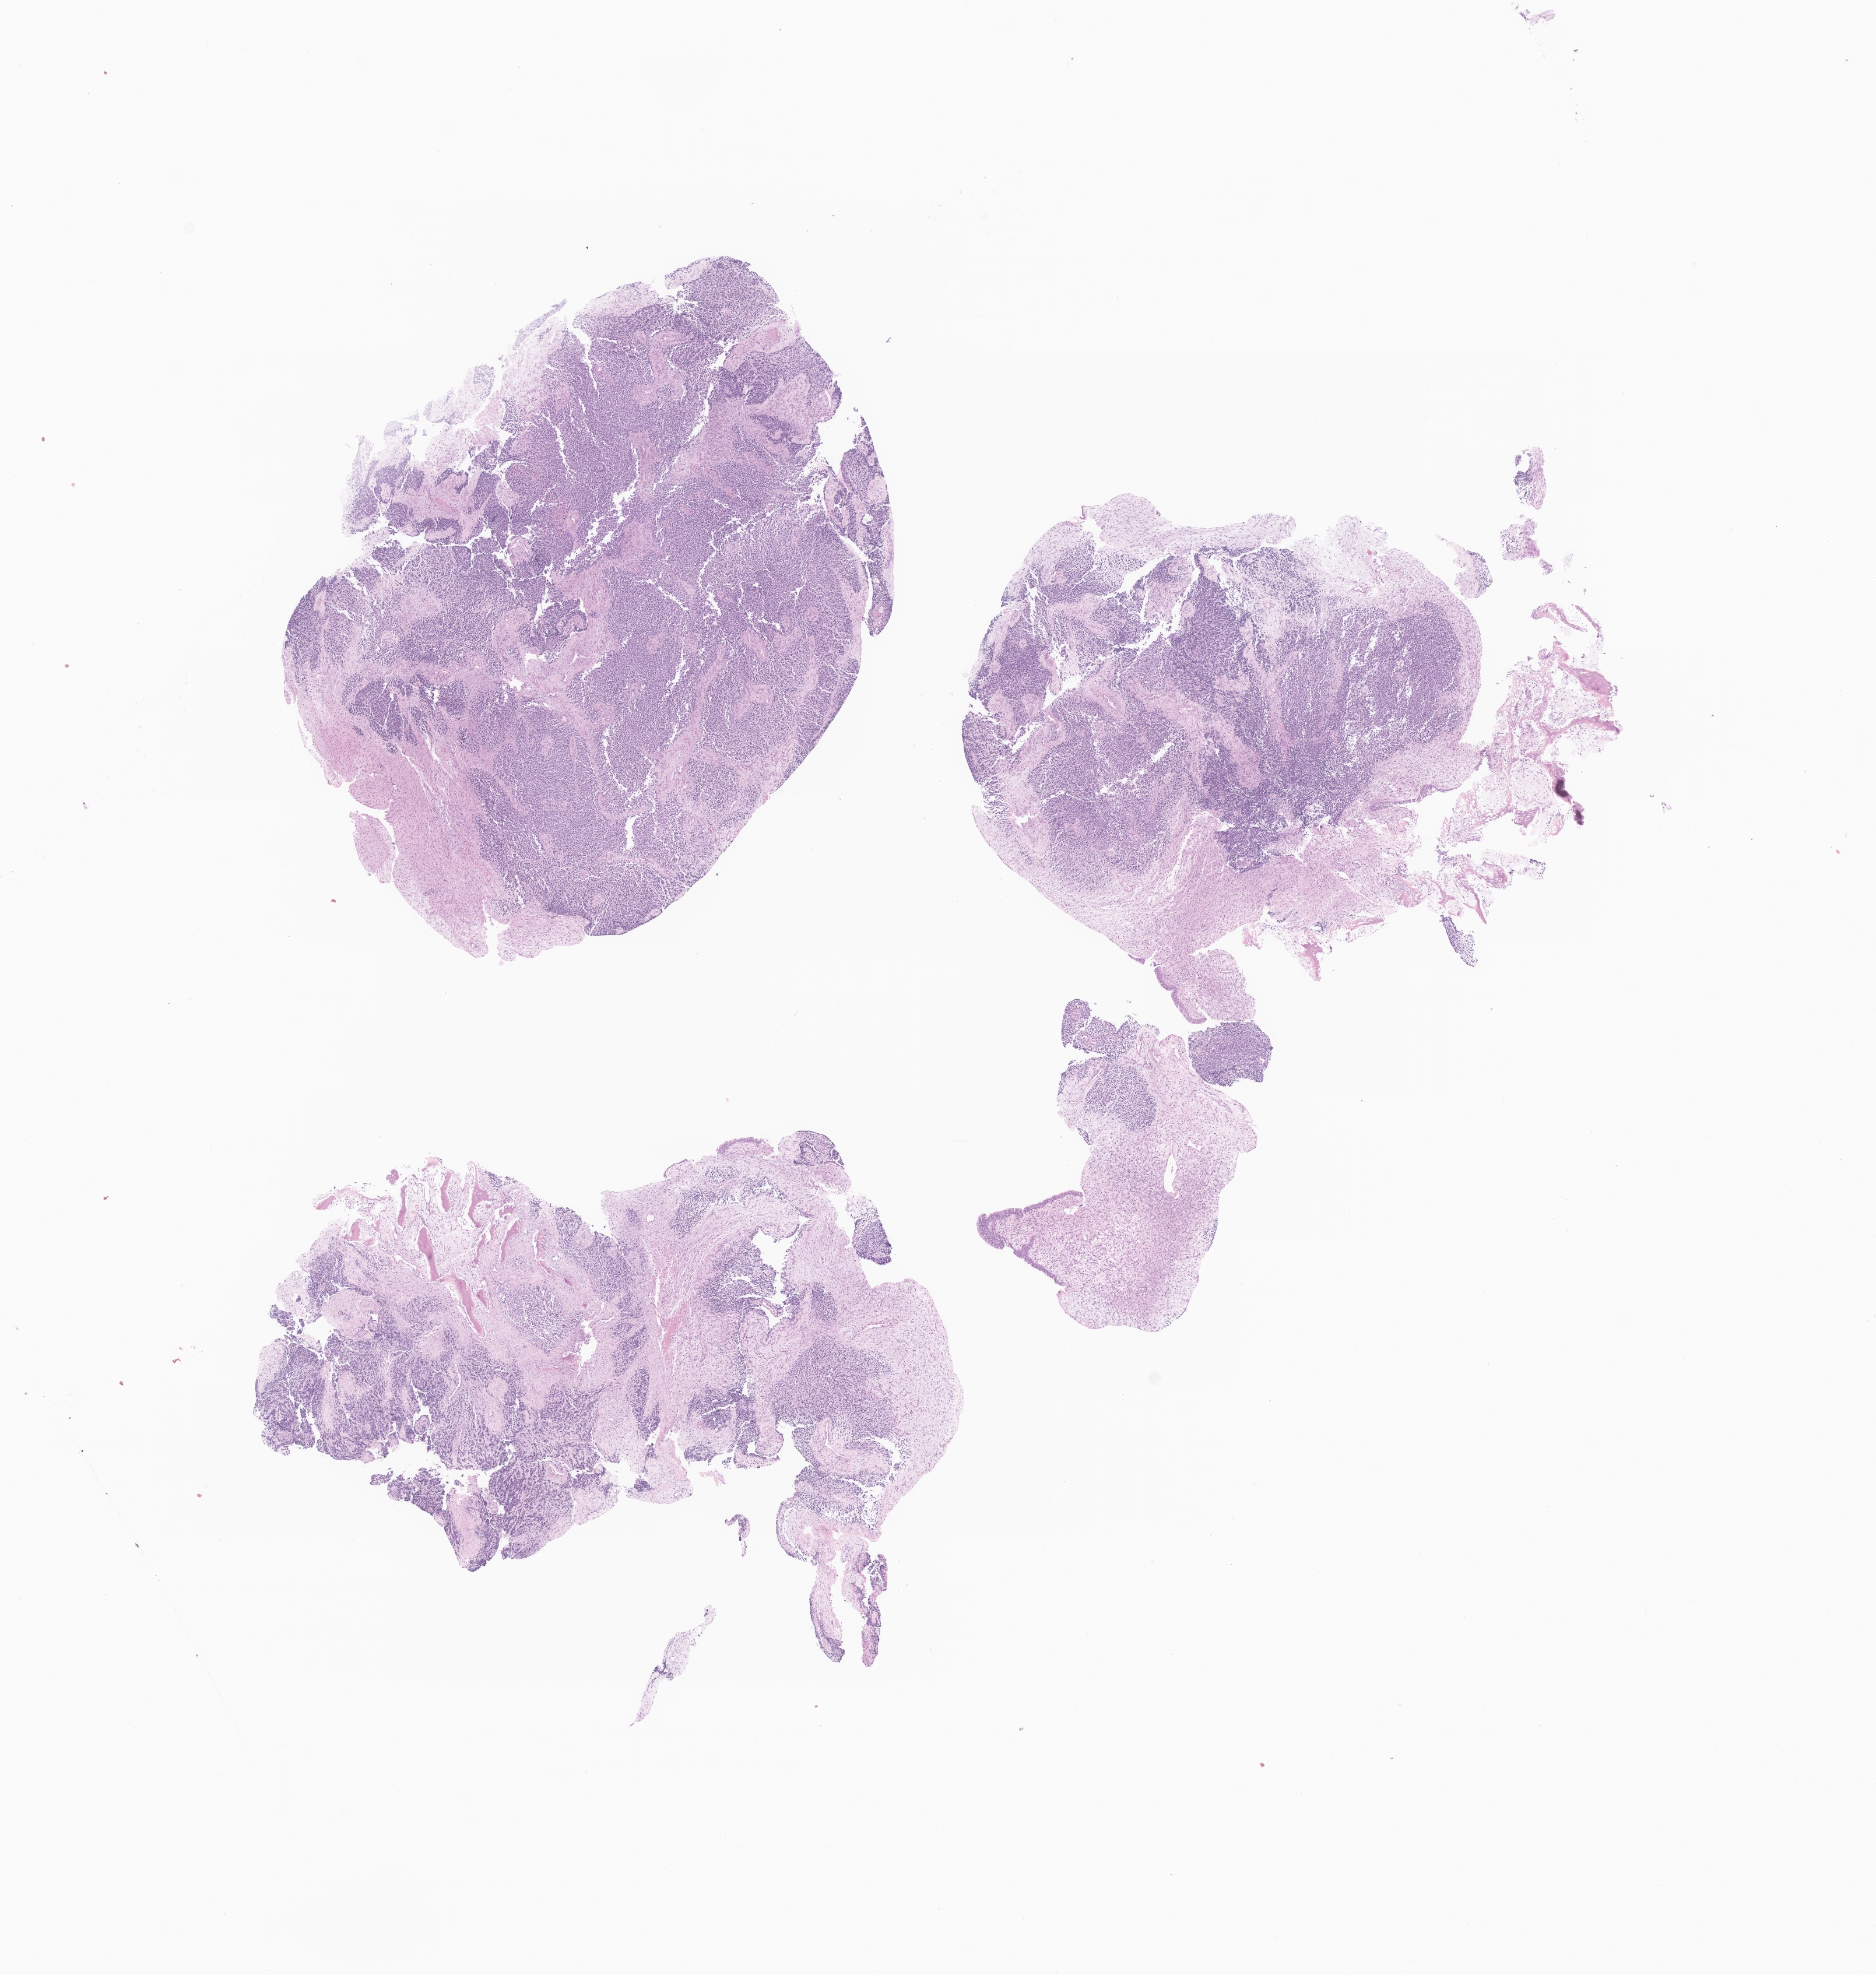
Digitized H&E-stained section of tumor tissue from the sphenoid sinus — shown as a low-resolution overview of the whole scanned area (about 13.6 x 14.3 mm), formalin-fixed paraffin-embedded section. Patient: female, age 148 months.
- diagnosis (ICD-O-3 morphology term): Embryonal rhabdomyosarcoma, NOS